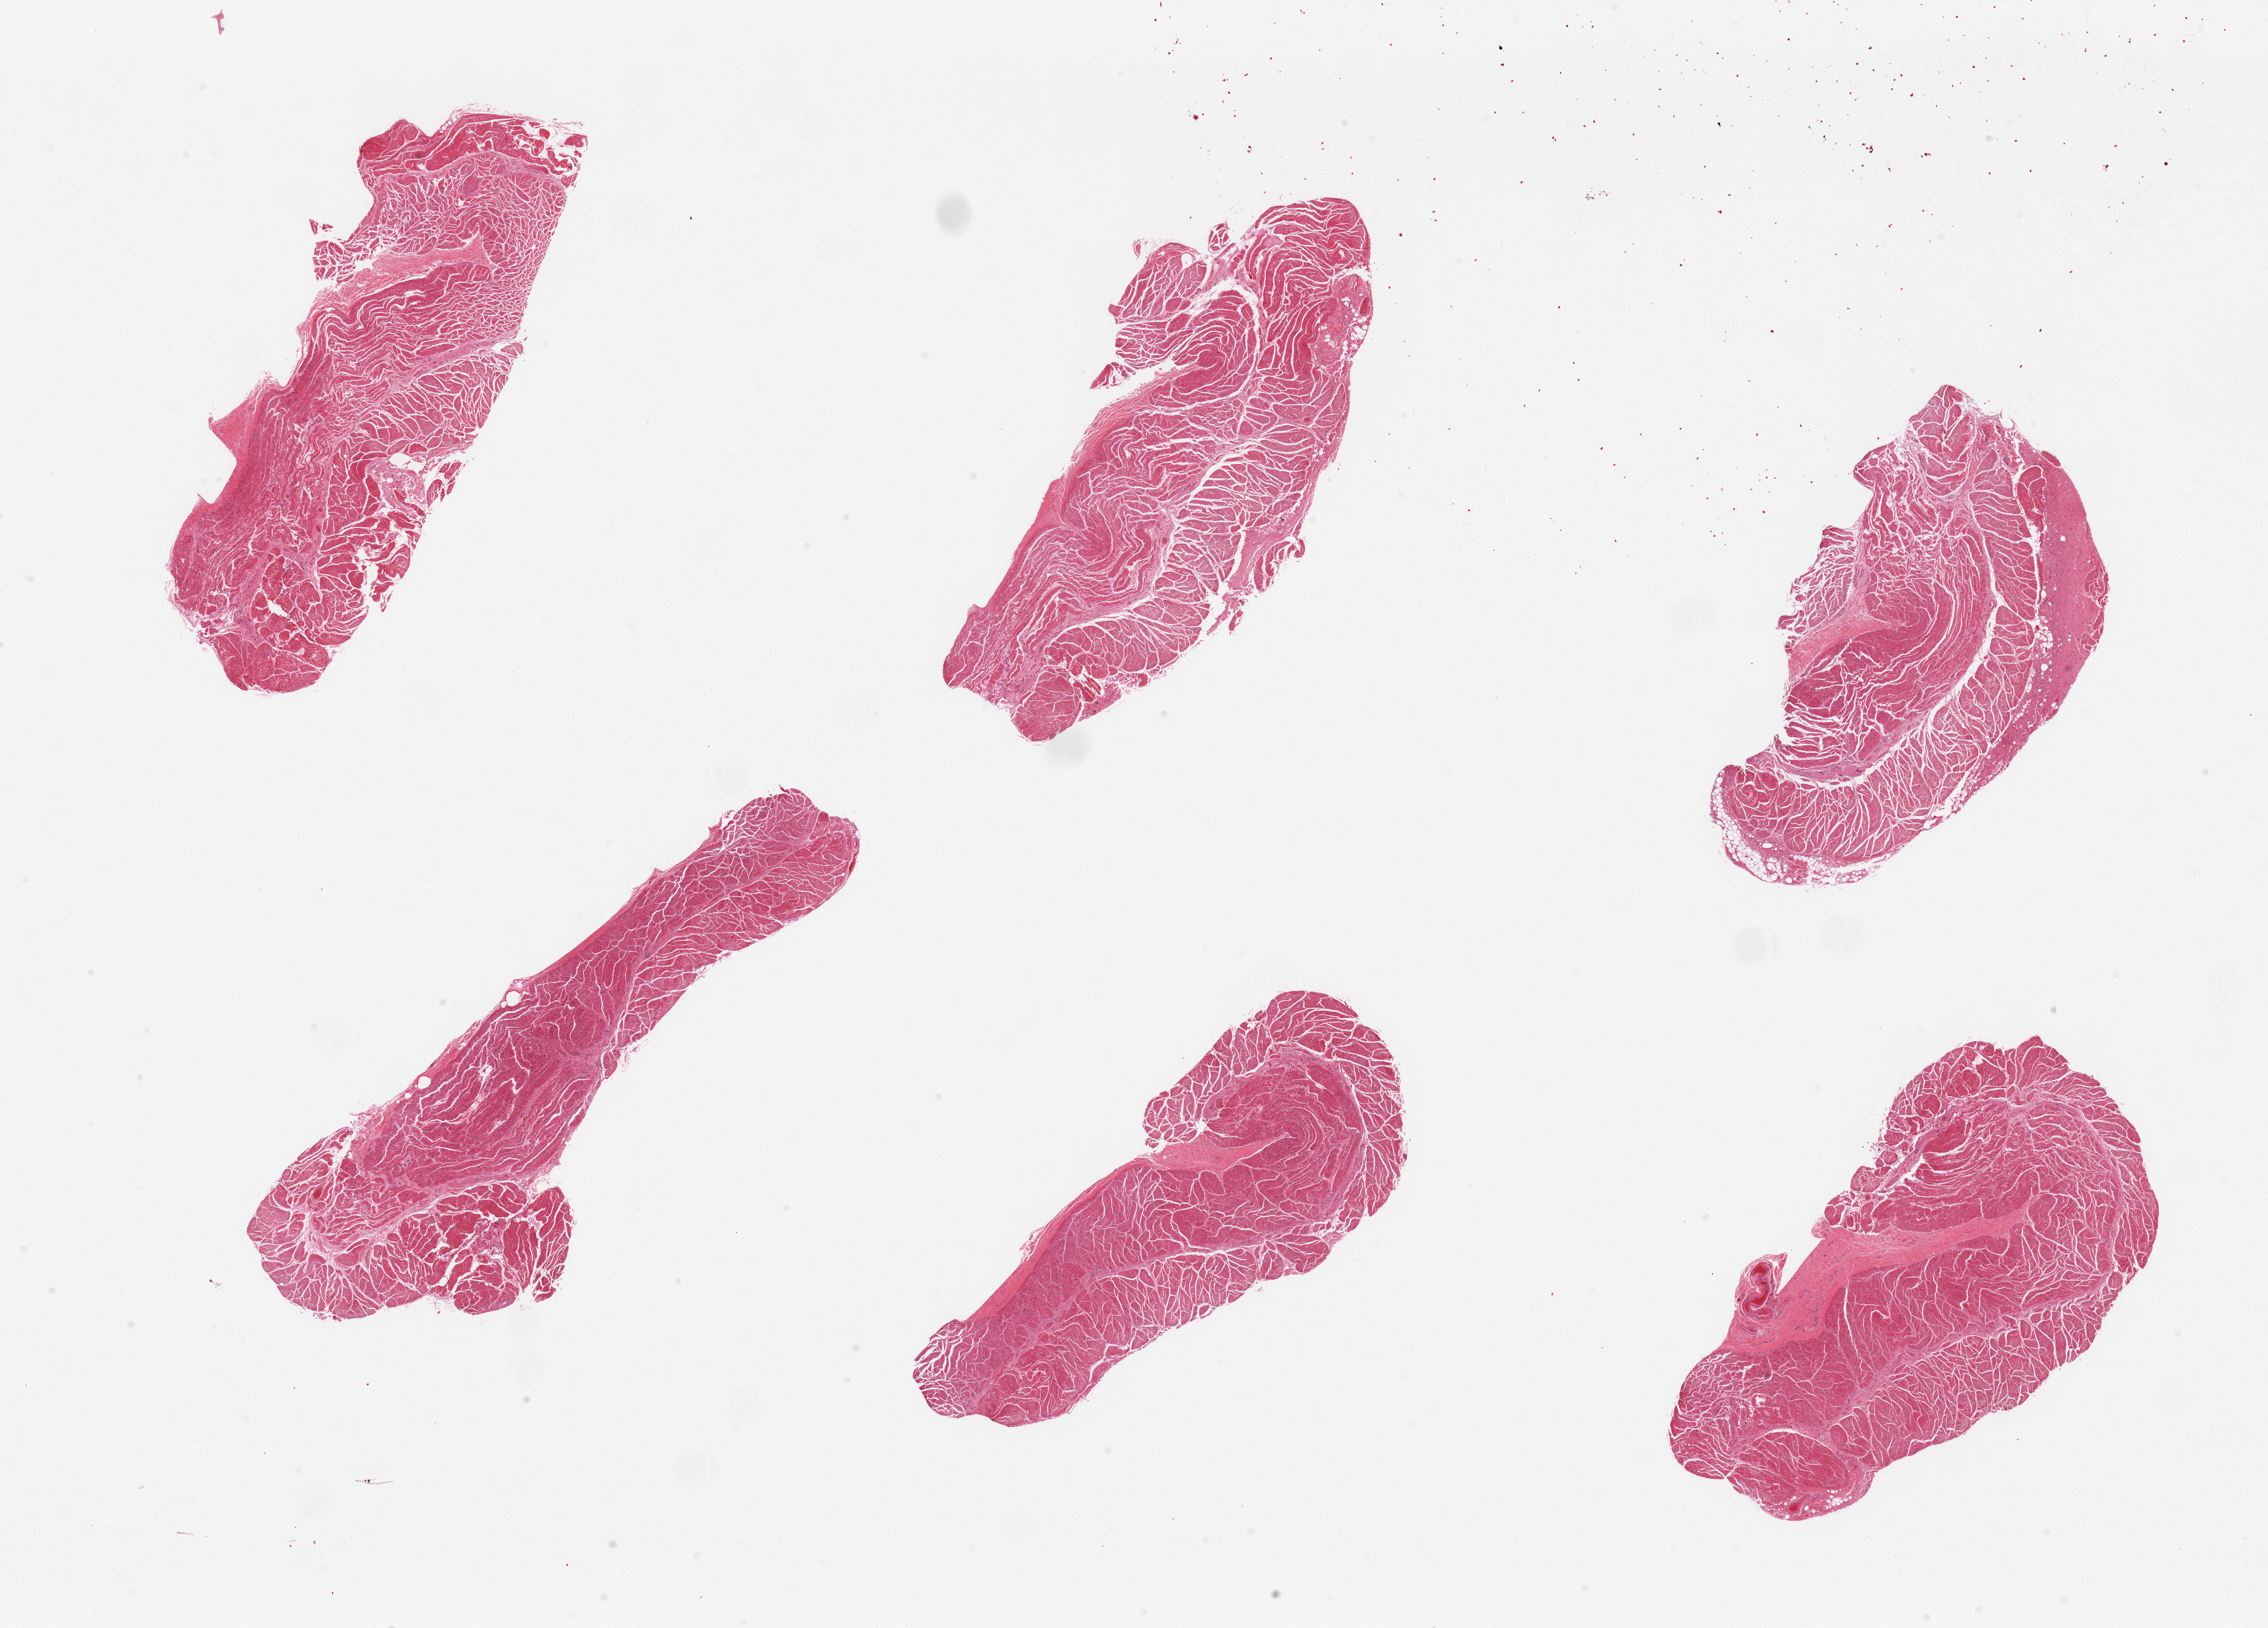
Digitized H&E-stained section, brightfield — low-resolution overview of the scanned area, about 31.5 x 22.6 mm (acquisition: 20x scan). PAXgene-fixed paraffin-embedded (PFPE) section. Sampled site (target tissue): esophageal muscle. Donor tissue sample. Donor sex: male.
Reviewer comment on this tissue sample: 6 pieces, all muscularis, good specimens.